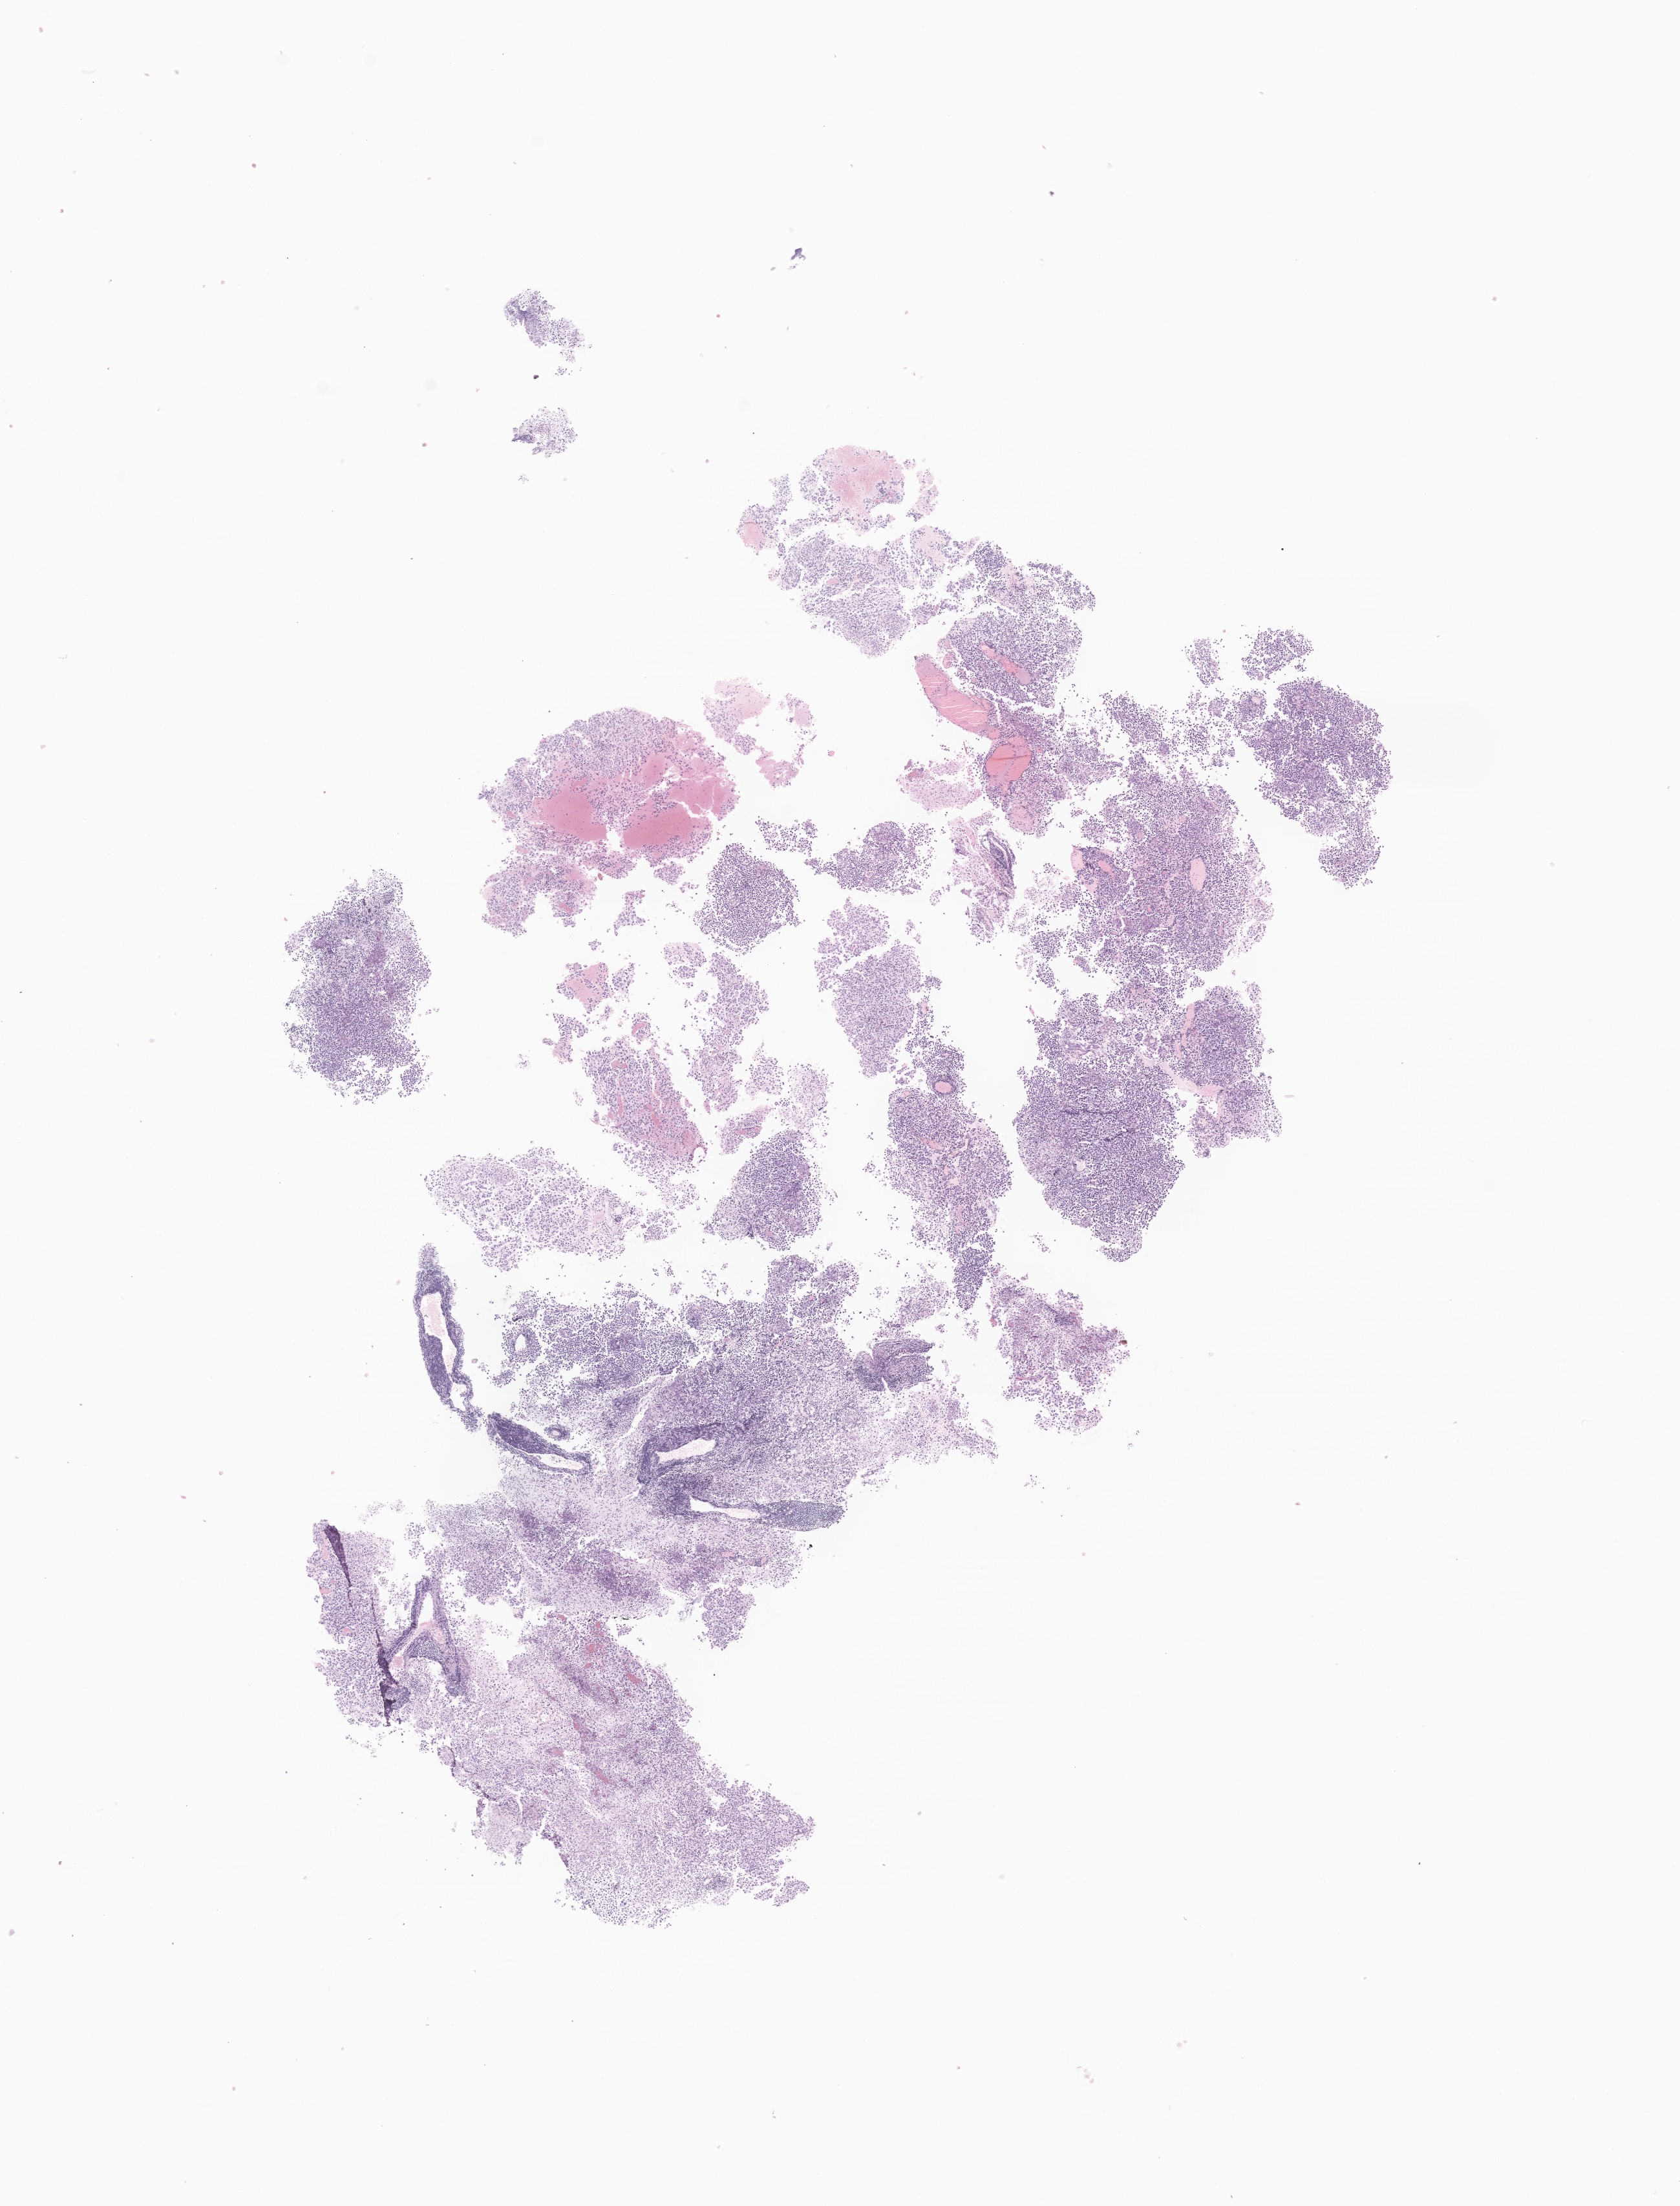
Haematoxylin and eosin whole-slide image of tumor tissue from the brain — shown as a low-resolution overview of the whole scanned area (about 11.0 x 14.4 mm). Formalin-fixed paraffin-embedded section. Male patient, age 200 months (16 years 8 months).
Diagnosis: Germinoma.